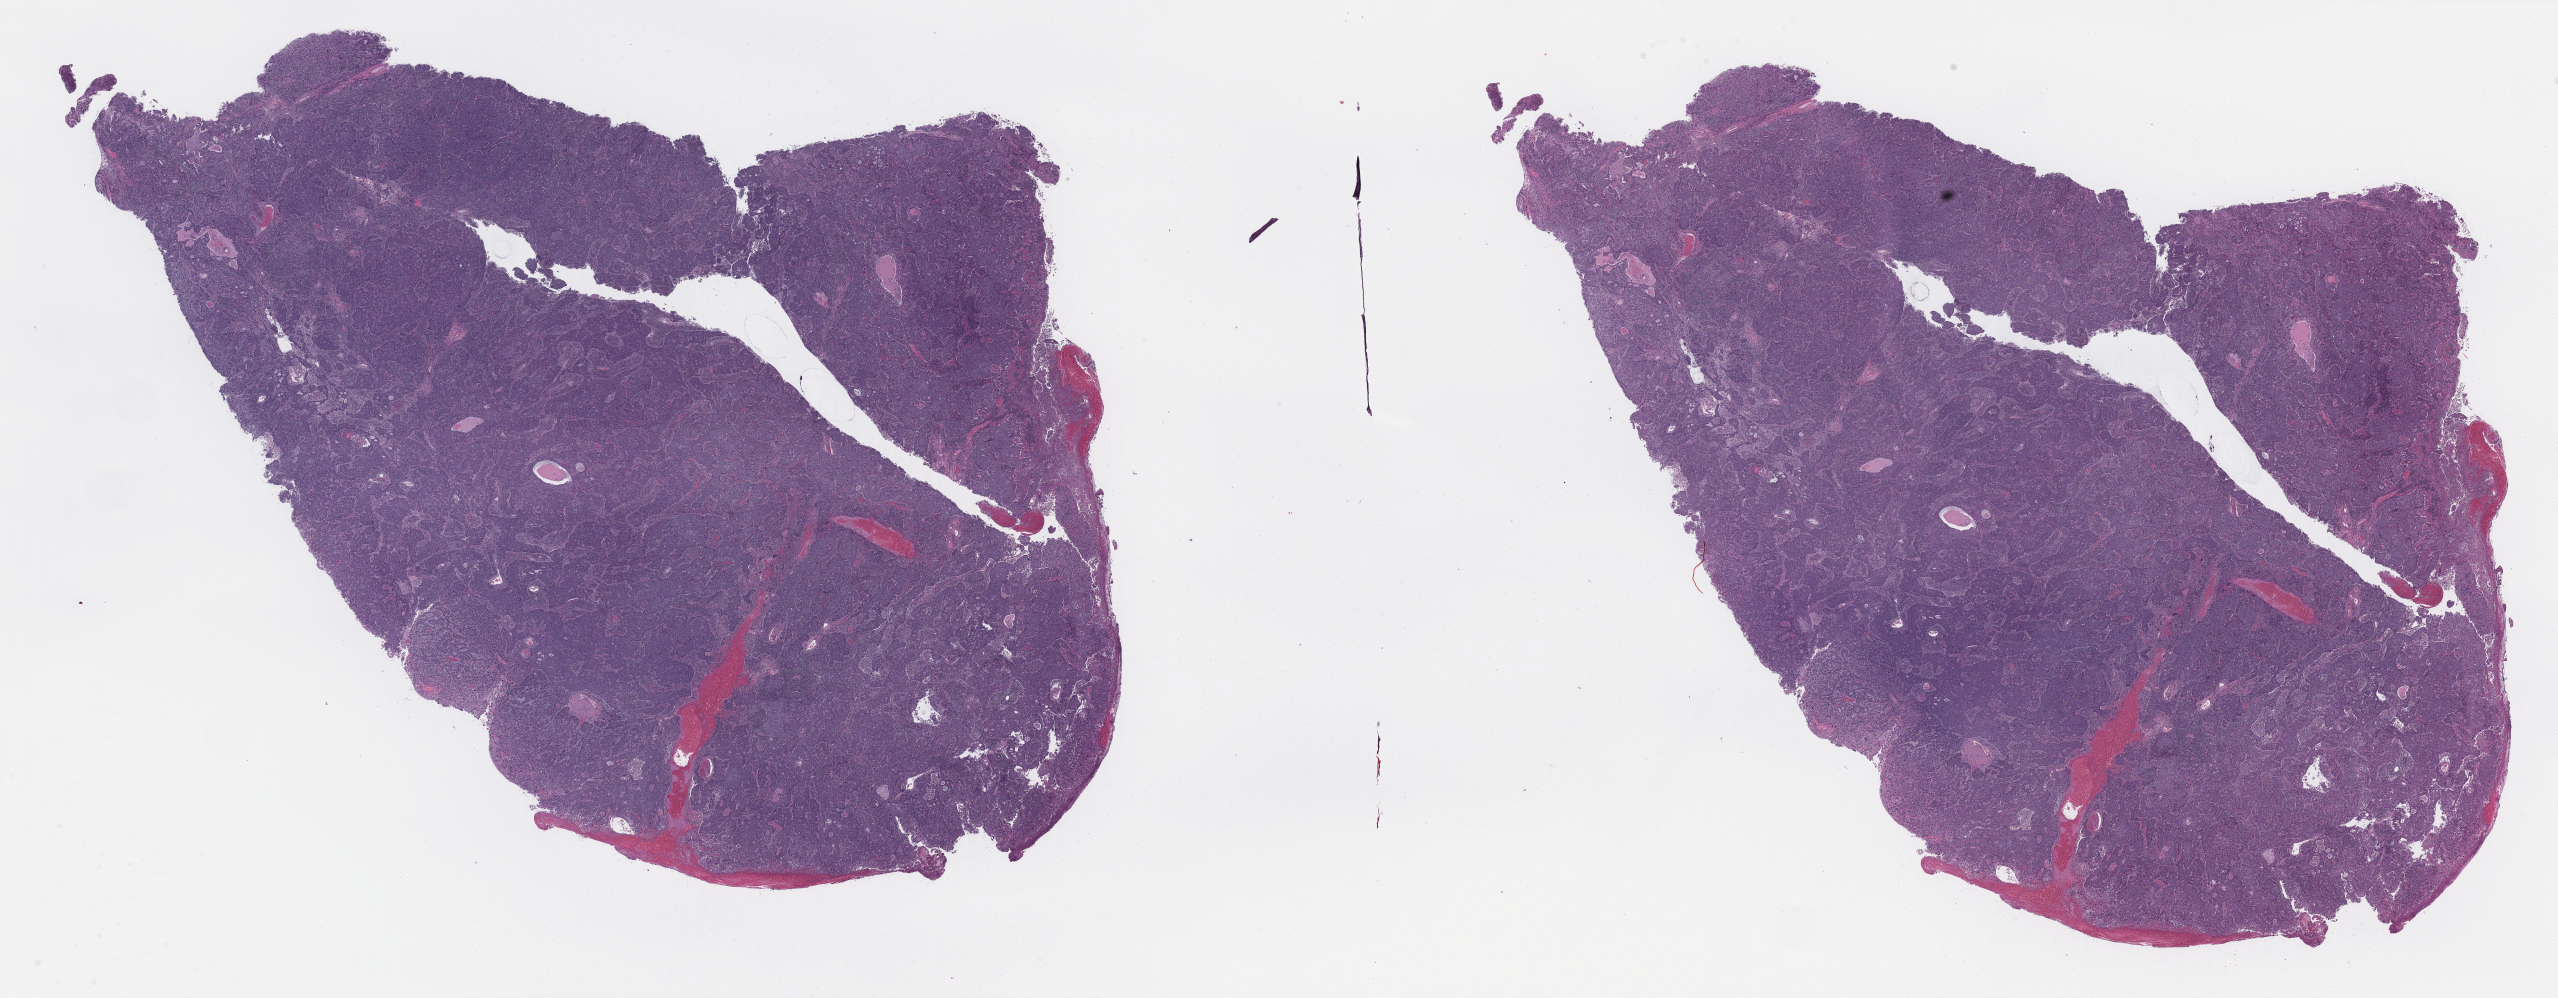
H&E-stained whole-slide image, a low-resolution overview of the entire scanned area, about 40.5 x 15.8 mm (acquisition: 40x scan), formalin-fixed paraffin-embedded (FFPE) diagnostic section, cervix, primary tumour sample. Female, age 44 years at initial diagnosis.
Diagnosis: Squamous cell carcinoma, NOS (cervix uteri).